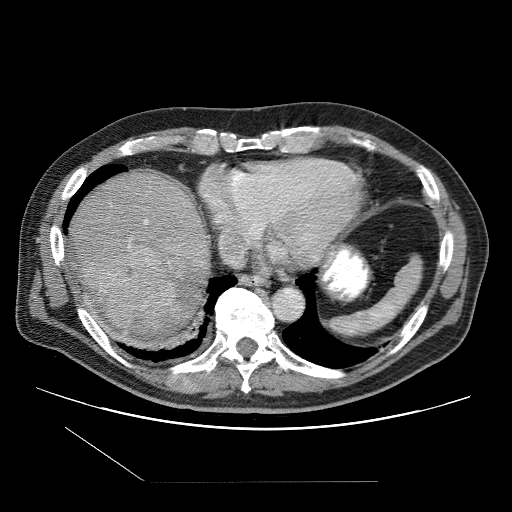
Contrast-enhanced abdominal CT (liver protocol), one axial slice; position 92 of 109 along the scan axis; reconstruction kernel STANDARD; one of 2 acquisitions stored at this slice position; soft-tissue window (W 400 / L 40 HU); 512 × 512 image matrix, field of view 400 × 400 mm. From the clinical record (not read from this slice): diagnosis: hepatocellular carcinoma (patient treated with transarterial chemoembolisation; whether this scan precedes or follows treatment is not stated here); TNM stage (as recorded): Stage-IIIB; Child-Pugh class: A; tumour differentiation: well differentiated; tumour nodularity: multinodular.
Structures marked on this image (semi-automatic segmentation, software-assisted and operator-edited):
- liver parenchyma outside the tumour (the mass and vessels are separate outlines, so this box may not span the whole liver): box from (x=66, y=172) to (x=208, y=340) px
- mass: (x=85, y=249)–(x=176, y=327)
- liver vessels: (x=129, y=220)–(x=148, y=248)